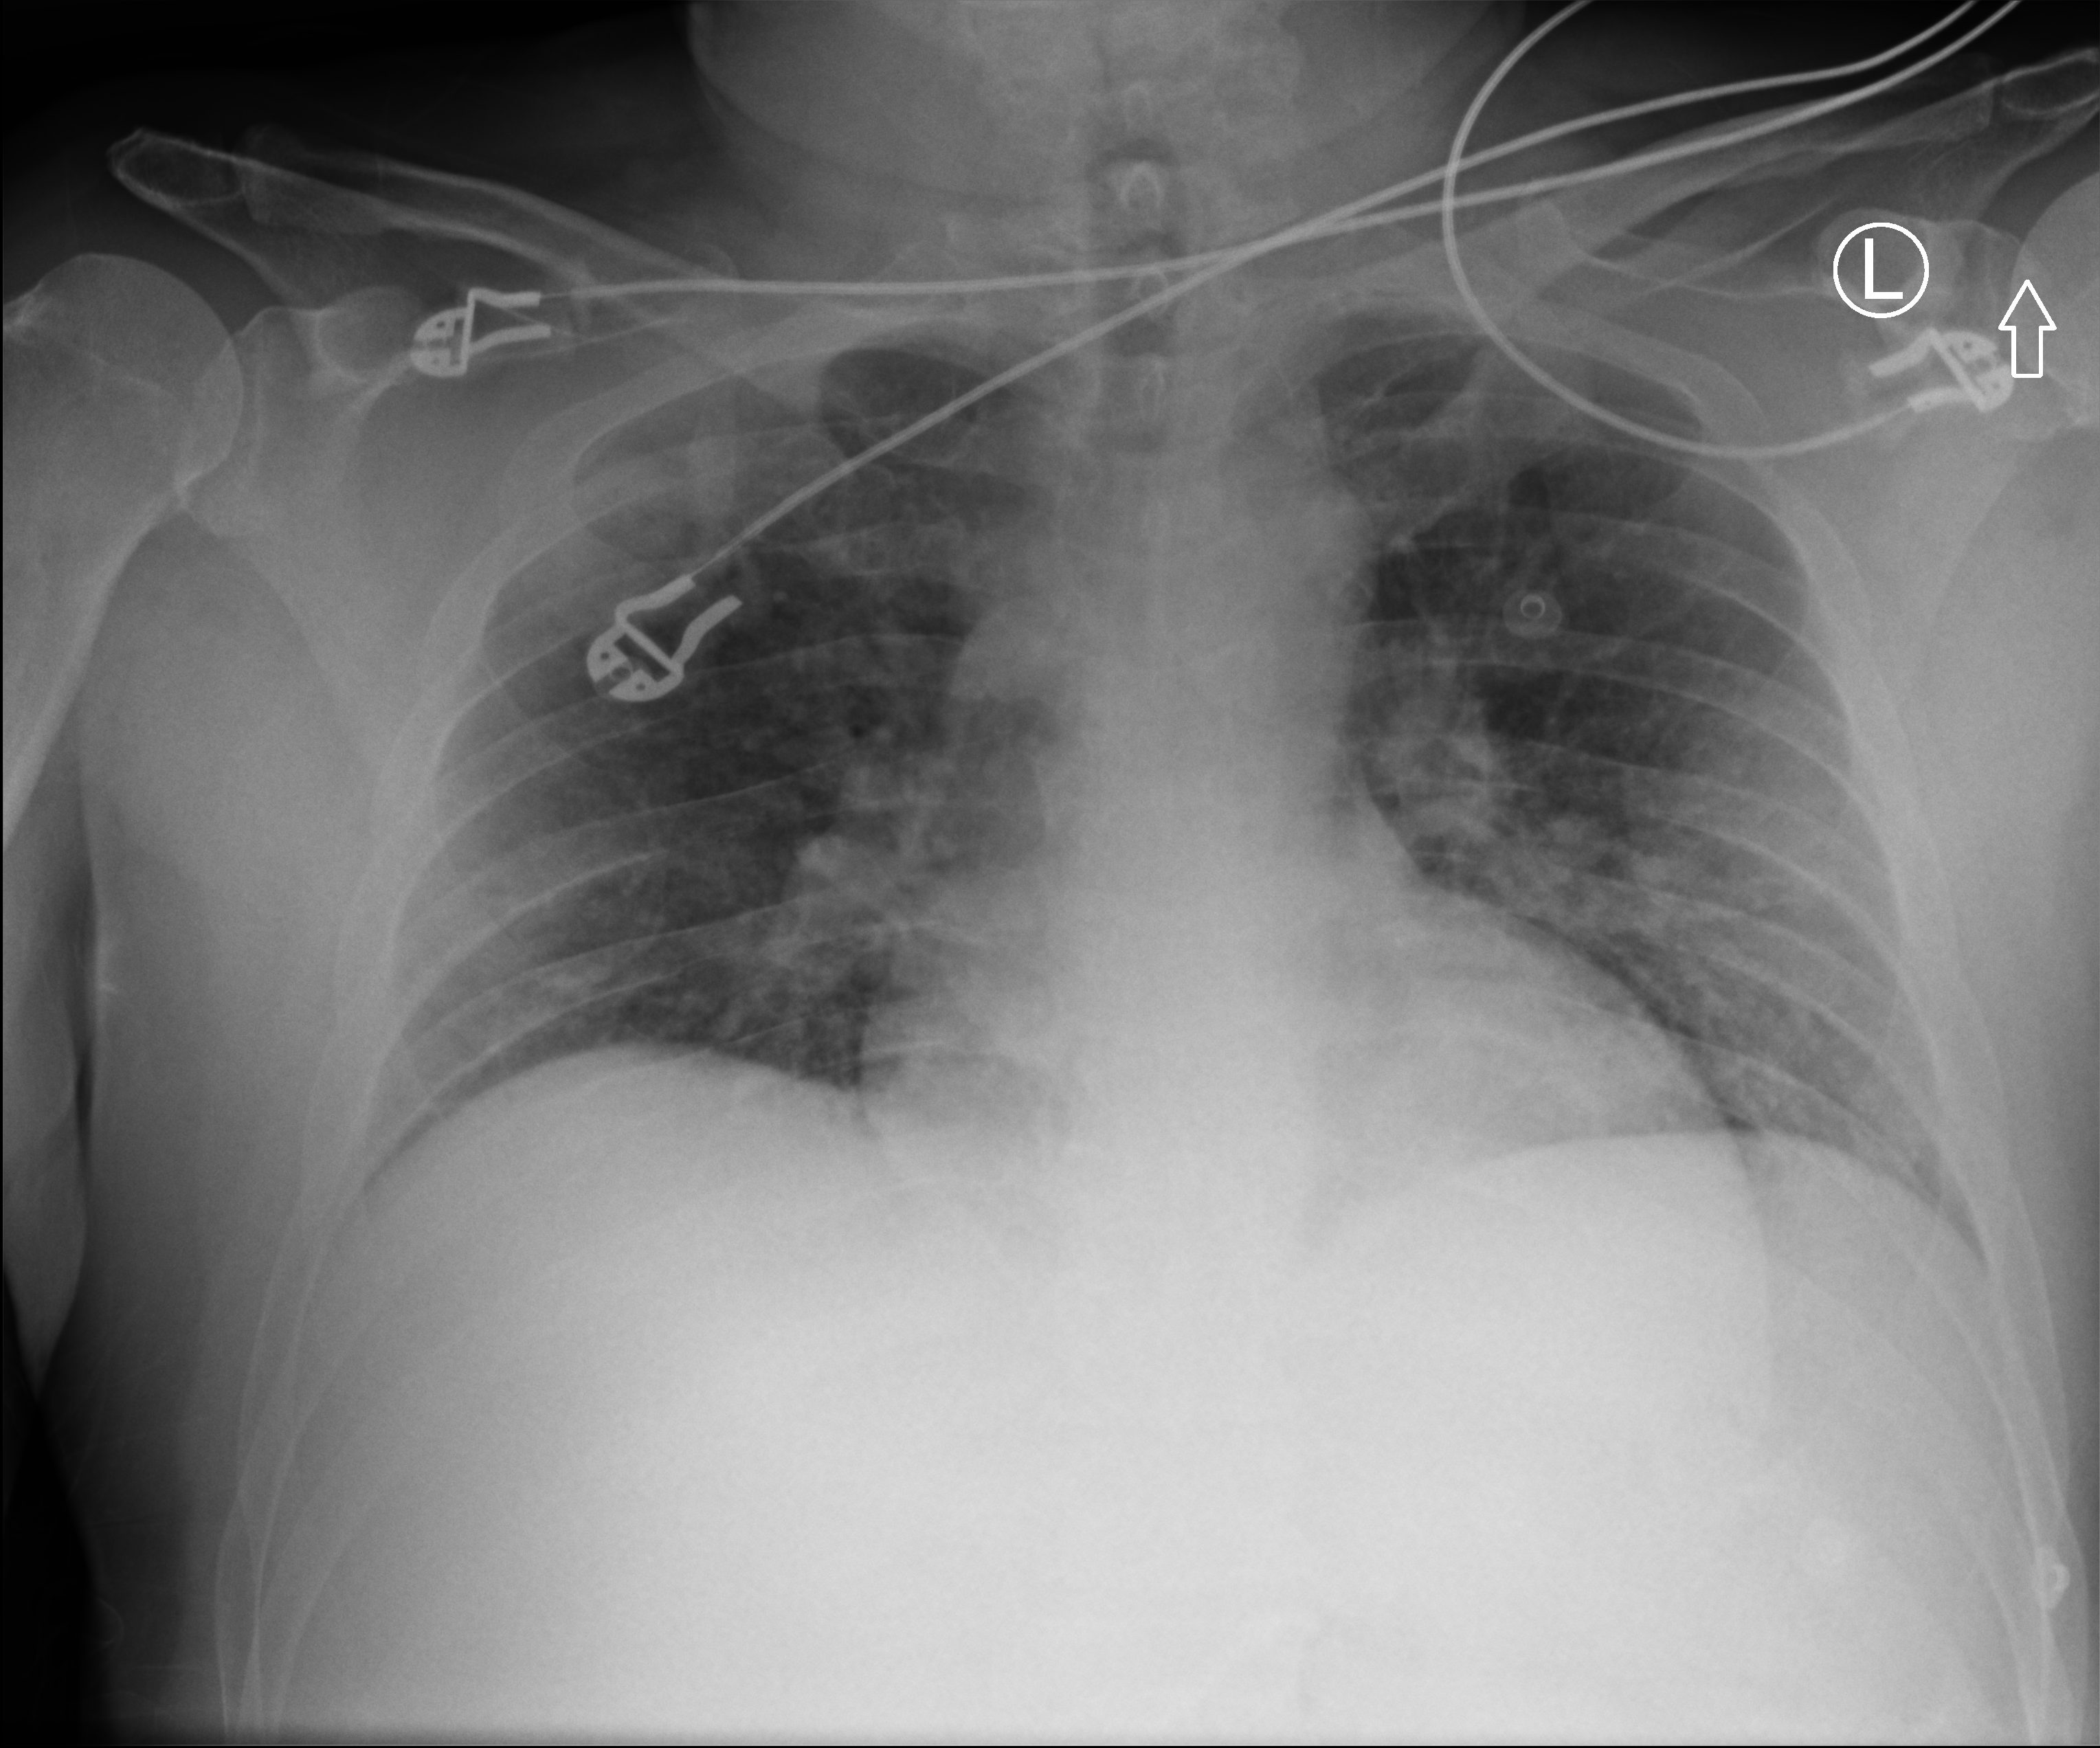
Chest X-ray (portable), anteroposterior (AP) projection. Patient hospitalised with COVID-19; male, aged 18–59 years.
From the hospital-stay record, not from the radiograph (when in the stay this image was taken is not recorded):
- hypertension (admission record): yes
- mechanically ventilated during this hospital stay: no
- admitted to intensive care during this hospital stay: no